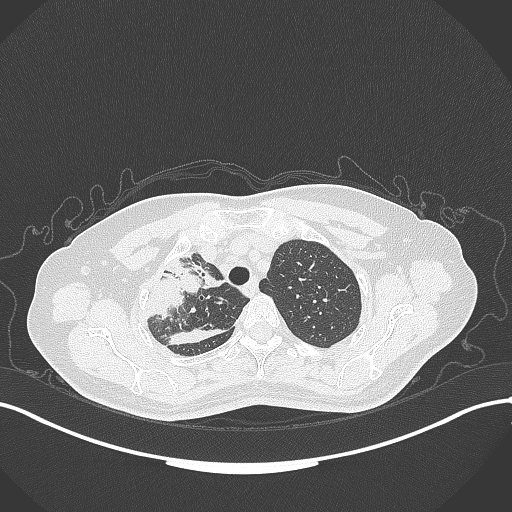
Chest CT, one axial slice. Position 261 of 309 along the scan axis. Lung window (W 1500 / L -600 HU). 1 mm slice thickness. 512 × 512 image matrix, field of view 400 × 400 mm. Female patient, age 60 years. From the clinical record (not read from this slice): clinical TNM (as recorded): T3 N1 M1.
Structures marked on this image (rectangle marked by the reading radiologist):
- lung tumour (recorded histology: adenocarcinoma): bounding box [x1, y1, x2, y2] px = [137, 255, 235, 323]